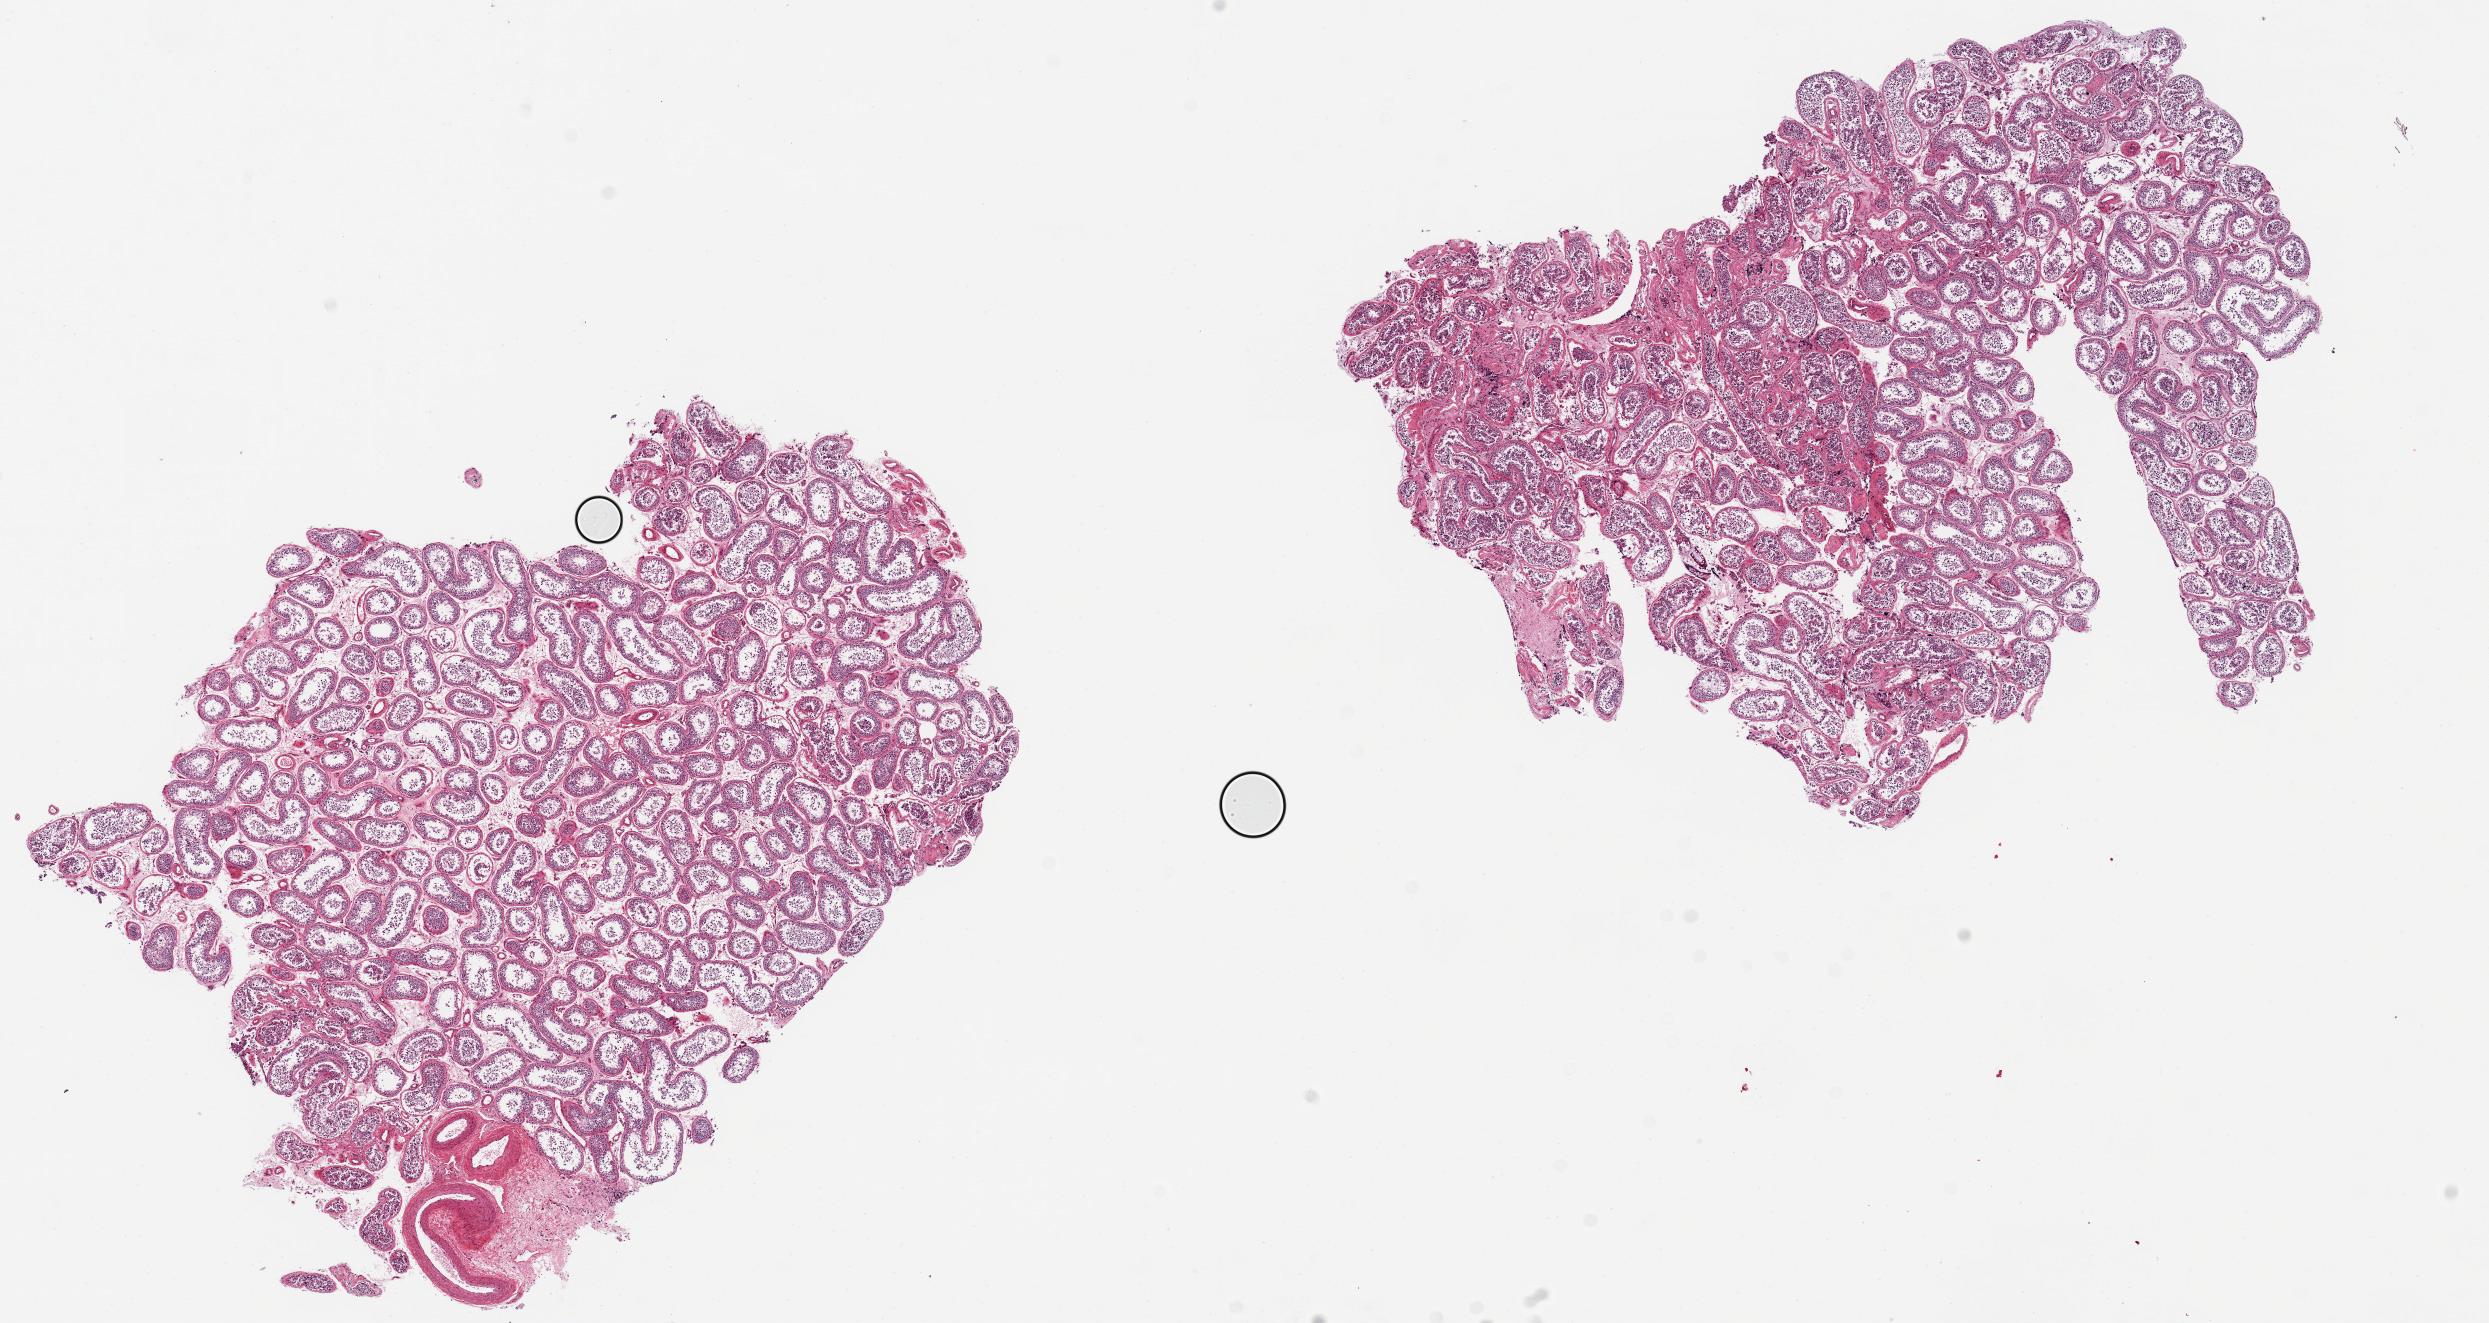
H&E whole-slide image — shown as a low-resolution overview of the whole scanned area (about 19.7 x 10.5 mm), PAXgene-fixed paraffin-embedded (PFPE) section, target tissue: testis, tissue donor sample. Donor sex: male.
Reviewer comment on this tissue sample: 2 pieces ~7x6mm, spermatogenesis is present; remarkably well preserved.